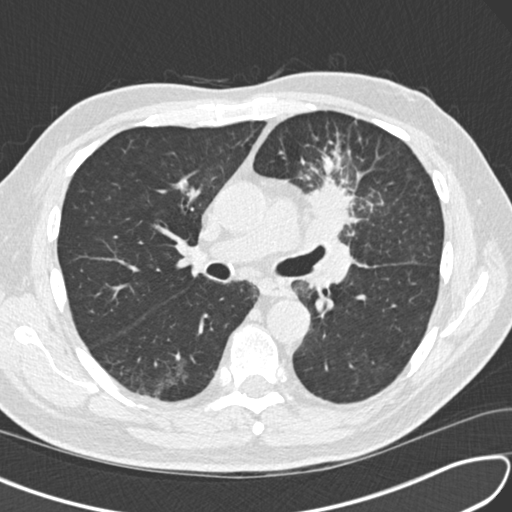
Low-dose screening chest CT, one axial slice; position 91 of 156 along the scan axis; reconstruction kernel B30f; 120 kVp; lung window (W 1500 / L -600 HU); 2 mm slice thickness; 512 × 512 image matrix, field of view 340 × 340 mm.
Annotated regions visible in this slice (outlined manually by an expert reader):
- lesion 1 (tumor, upper lobe of left lung): bounding box (x1, y1, x2, y2) in pixels: (309, 180, 352, 240)